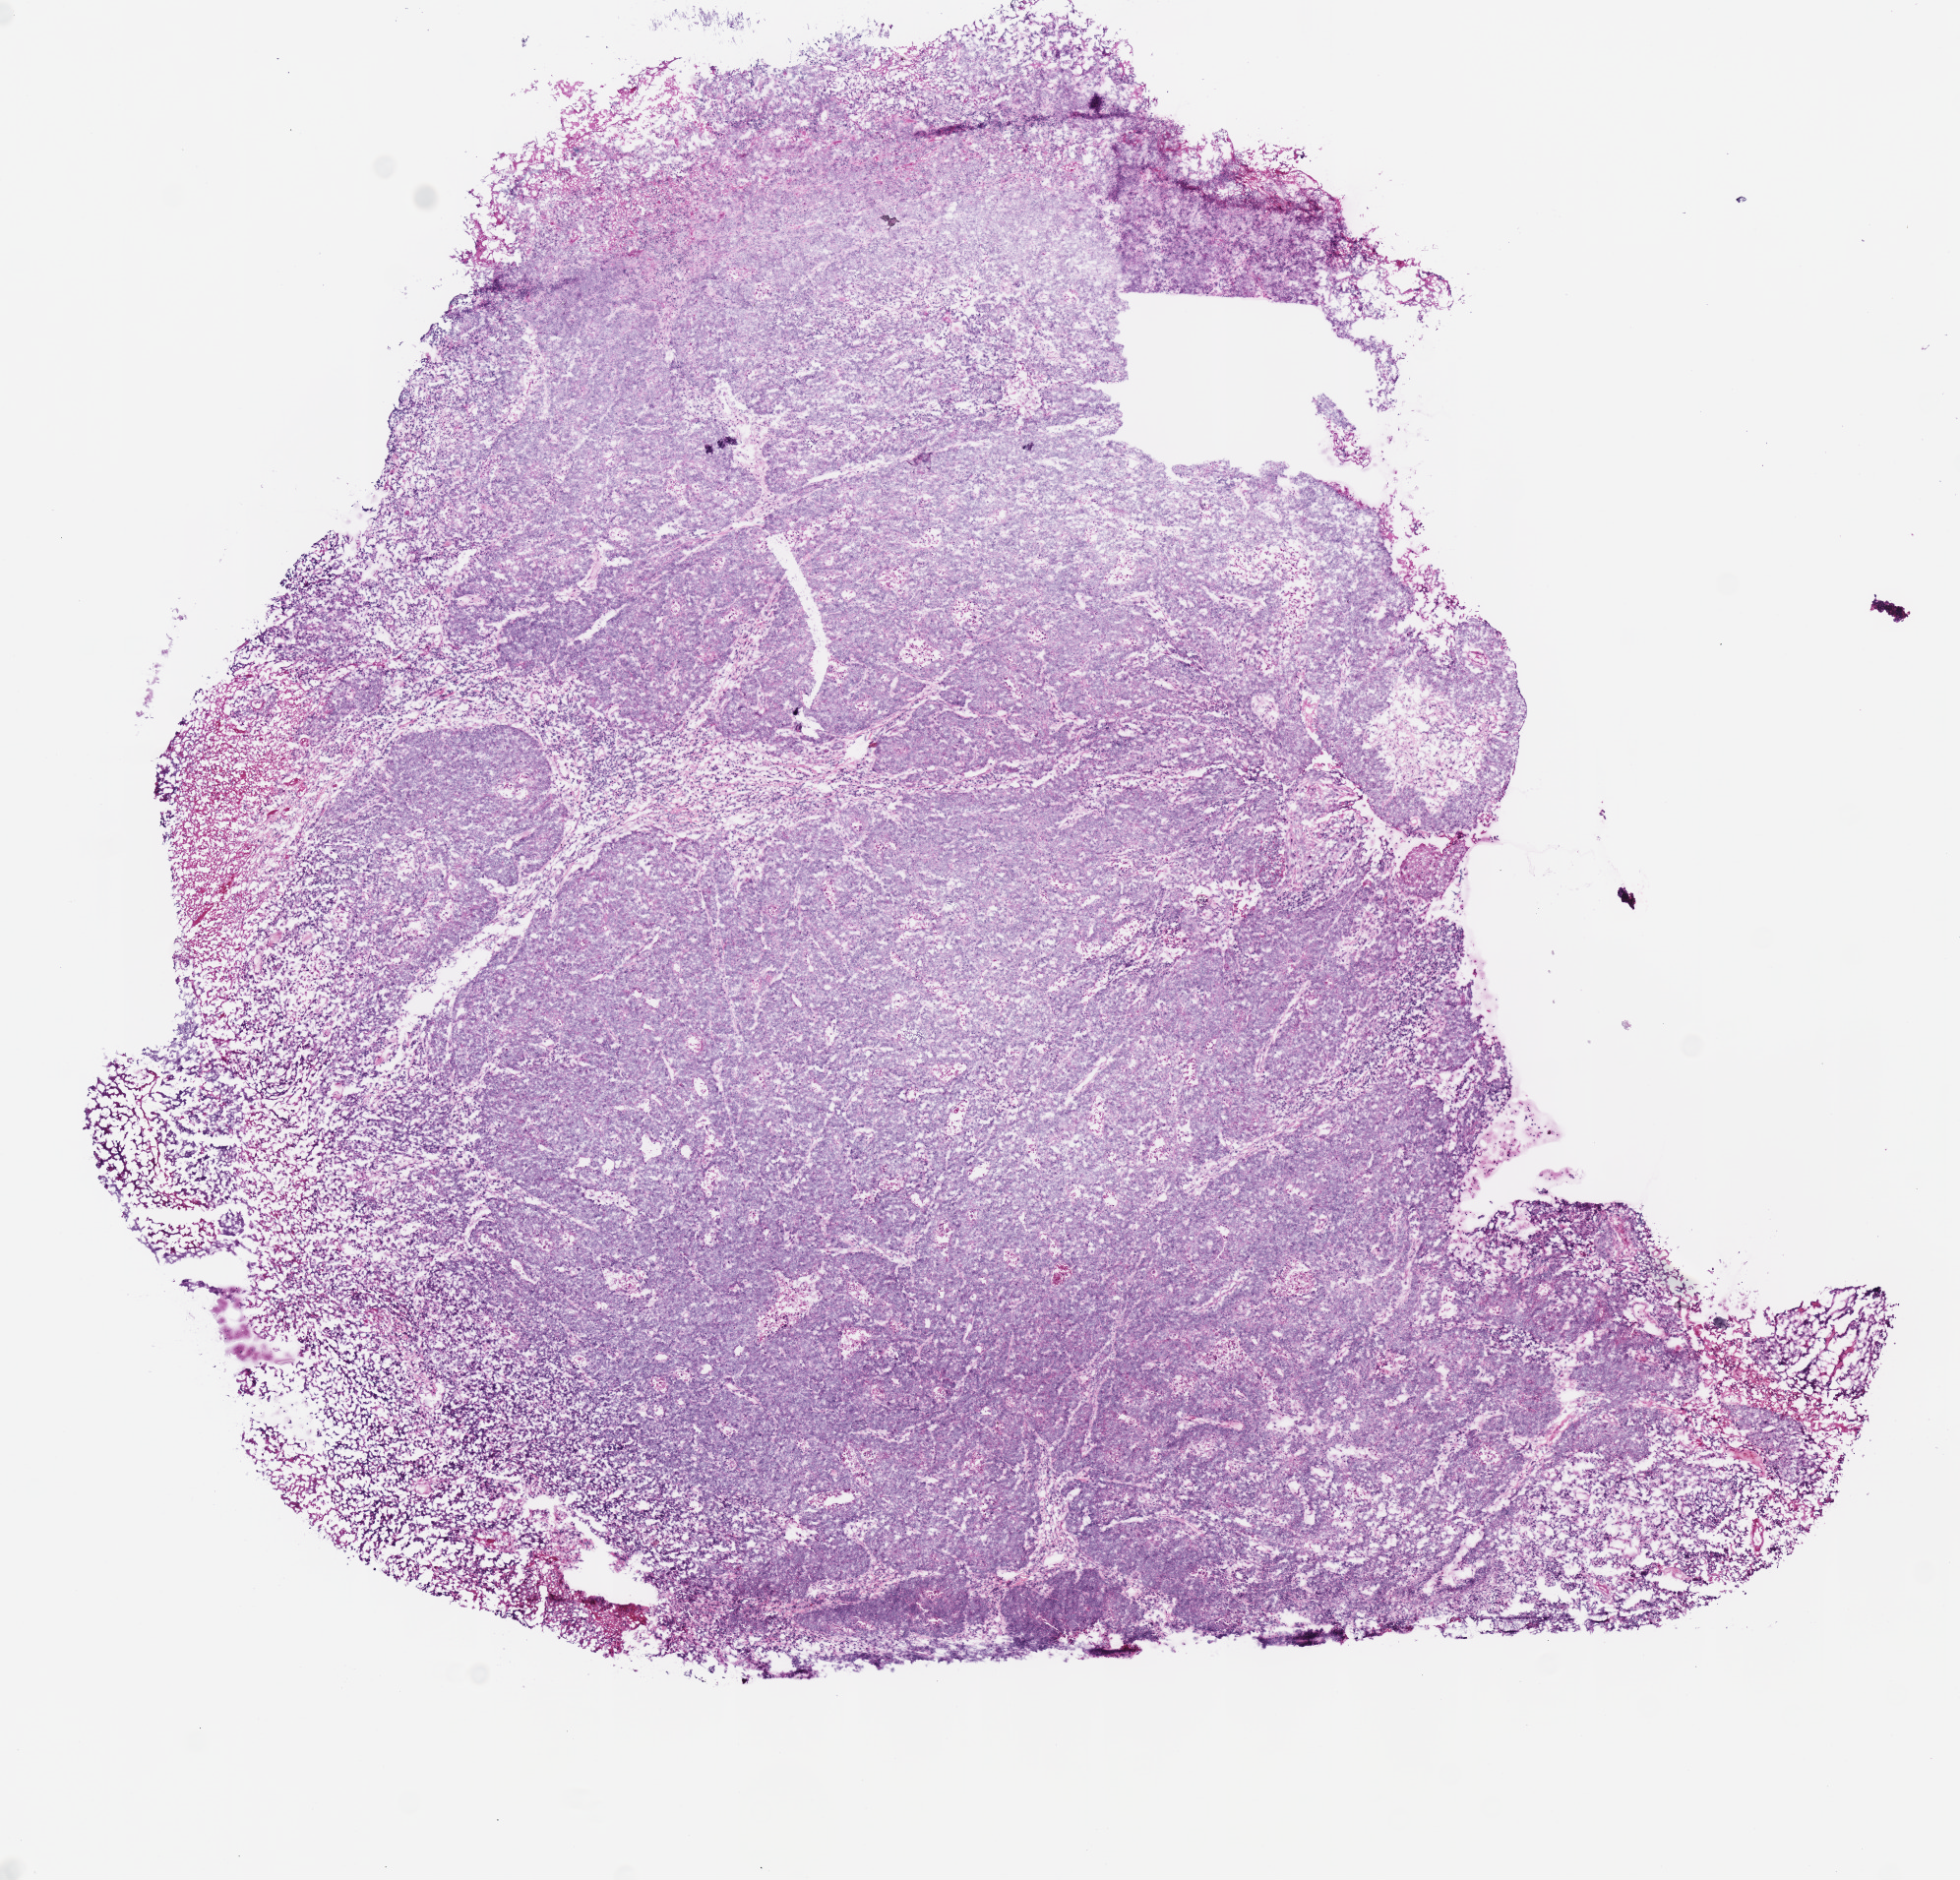
Whole-slide histology image, H&E-stained — low-resolution overview of the scanned area, about 7.8 x 7.5 mm (from a 40x scan). Frozen section from the top of the tissue portion. Sample: primary tumour, head and neck. Patient: male, age at initial diagnosis 40 years. Slide review estimates, as recorded: tumour cells 85%, tumour nuclei 80%.
Pathologic diagnosis: Squamous cell carcinoma, NOS.